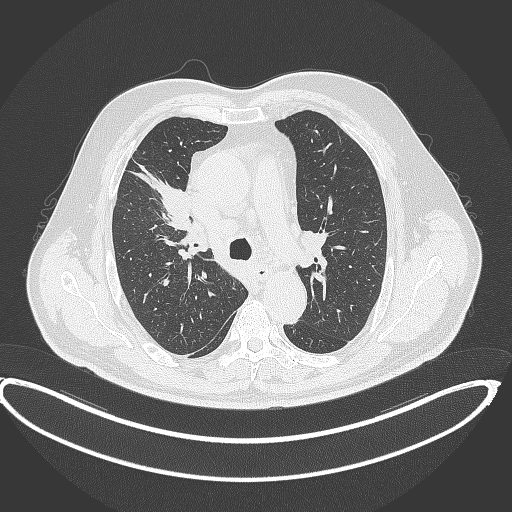
Chest CT, one axial slice. Slice 275 of 390 in the series (ordered by position). Reconstruction kernel B70f. 120 kVp. Lung window (W 1500 / L -600 HU). 512 × 512 image matrix. Patient: male, 62 years. From the clinical record (not read from this slice): clinical TNM (as recorded): T1c N3 M1c.
Annotated regions visible in this slice (bounding box drawn by a radiologist):
- lung tumour (recorded histology: adenocarcinoma): bounding box (x1, y1, x2, y2) in pixels: (151, 179, 190, 230)